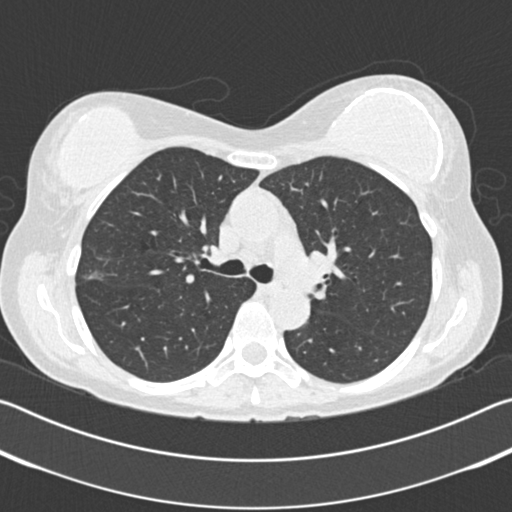
Low-dose screening chest CT, one axial slice. Position 121 of 183 along the scan axis. Lung window (W 1500 / L -600 HU). 512 × 512 image matrix, field of view 340 × 340 mm.
Structures marked on this image (expert manual segmentation):
- lesion 1 (tumor, upper lobe of right lung): box from (x=83, y=270) to (x=104, y=281) px